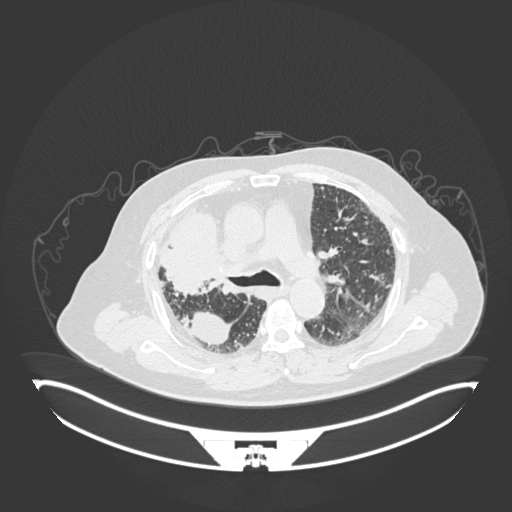
Chest CT, one axial slice. Position 116 of 201 along the scan axis. Reconstruction kernel B30f. 120 kVp. Lung window (W 1500 / L -600 HU). 1 mm slice thickness. 512 × 512 image matrix. Patient: male, 69 years. From the clinical record (not read from this slice): clinical TNM (as recorded): T4 N3 M1.
Structures marked on this image (rectangle marked by the reading radiologist):
- lung tumour (recorded histology: adenocarcinoma): box from (x=156, y=206) to (x=226, y=295) px